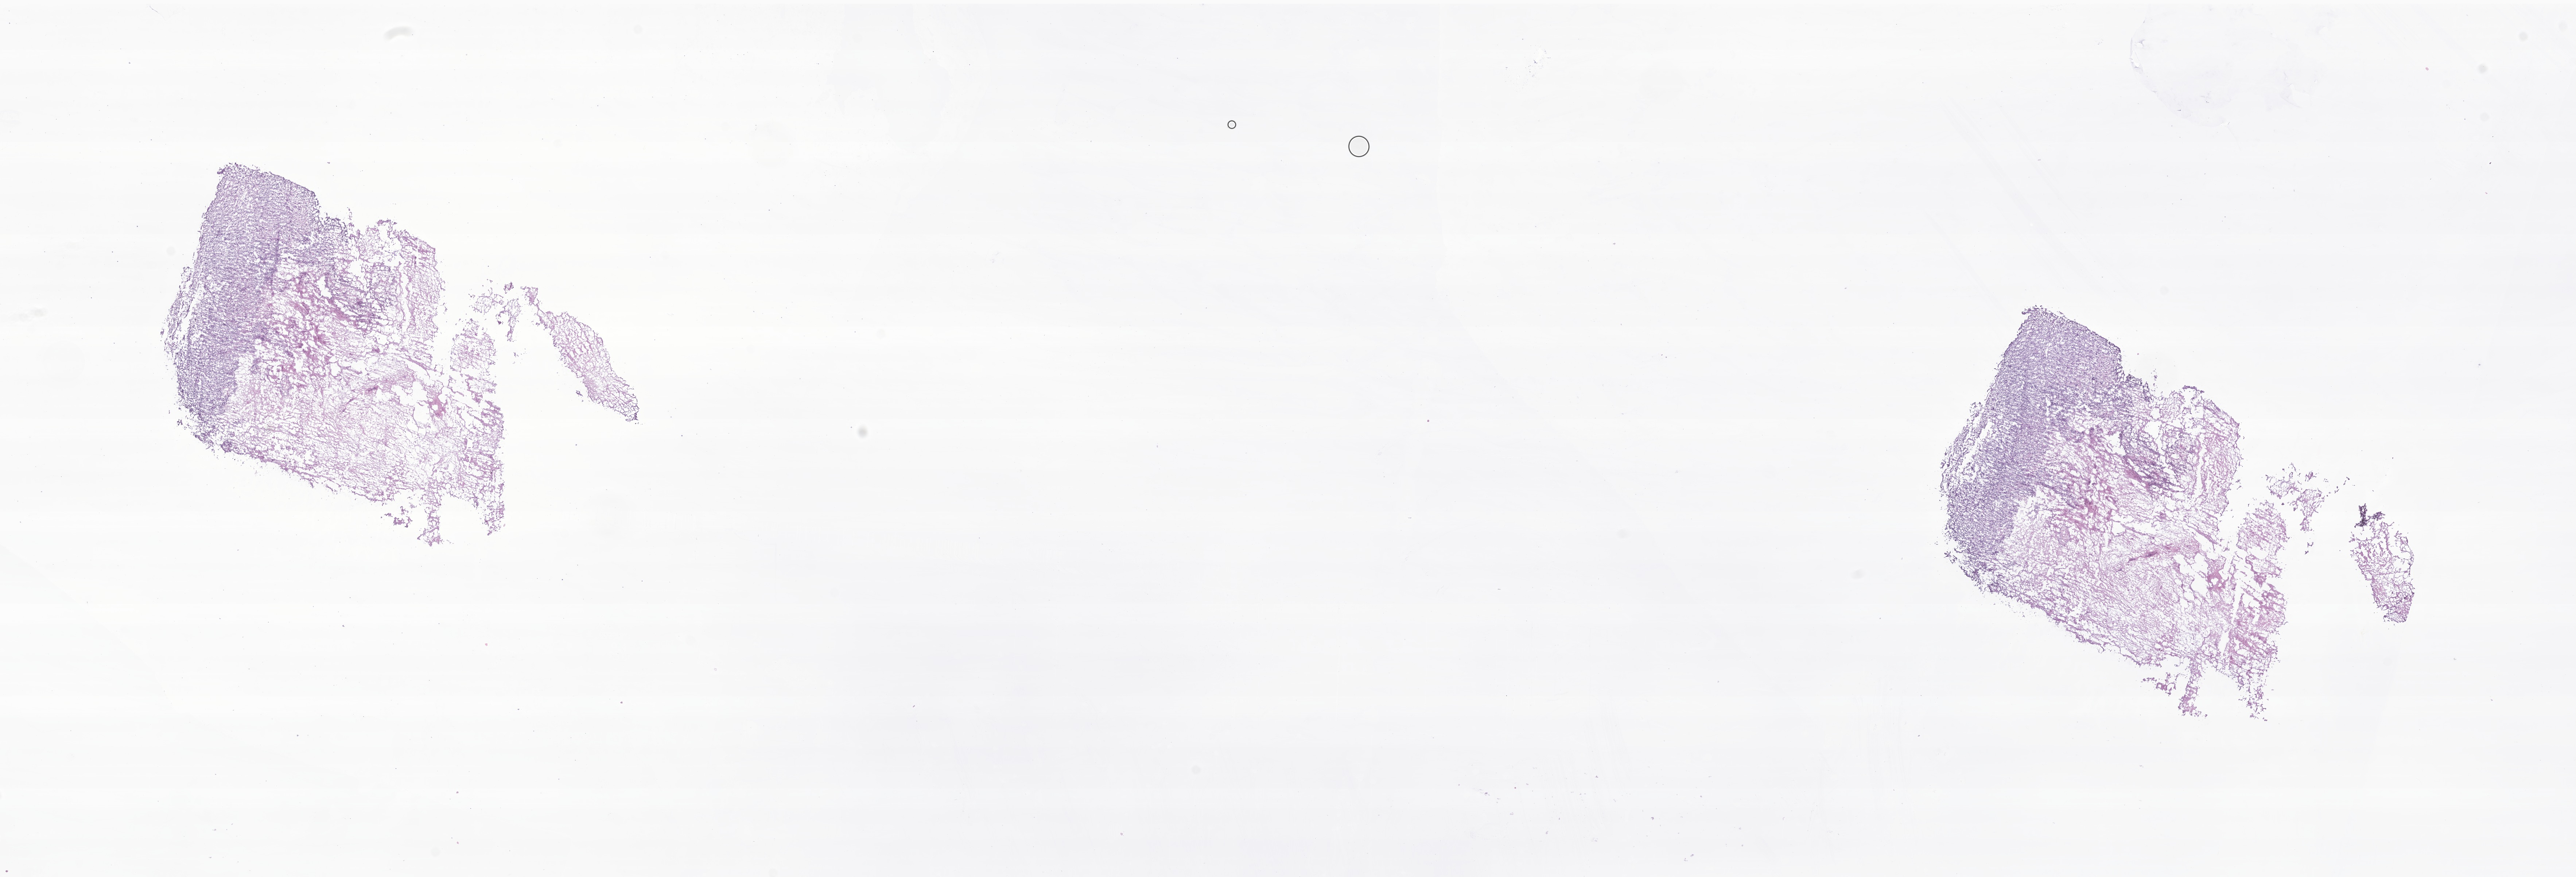
Digitized haematoxylin and eosin-stained section of tumor tissue from the brain — a low-resolution overview of the entire scanned area, about 29.8 x 10.1 mm. Frozen section. Male patient, age 210 months (17 years 6 months).
Diagnosis: Glioma, malignant.